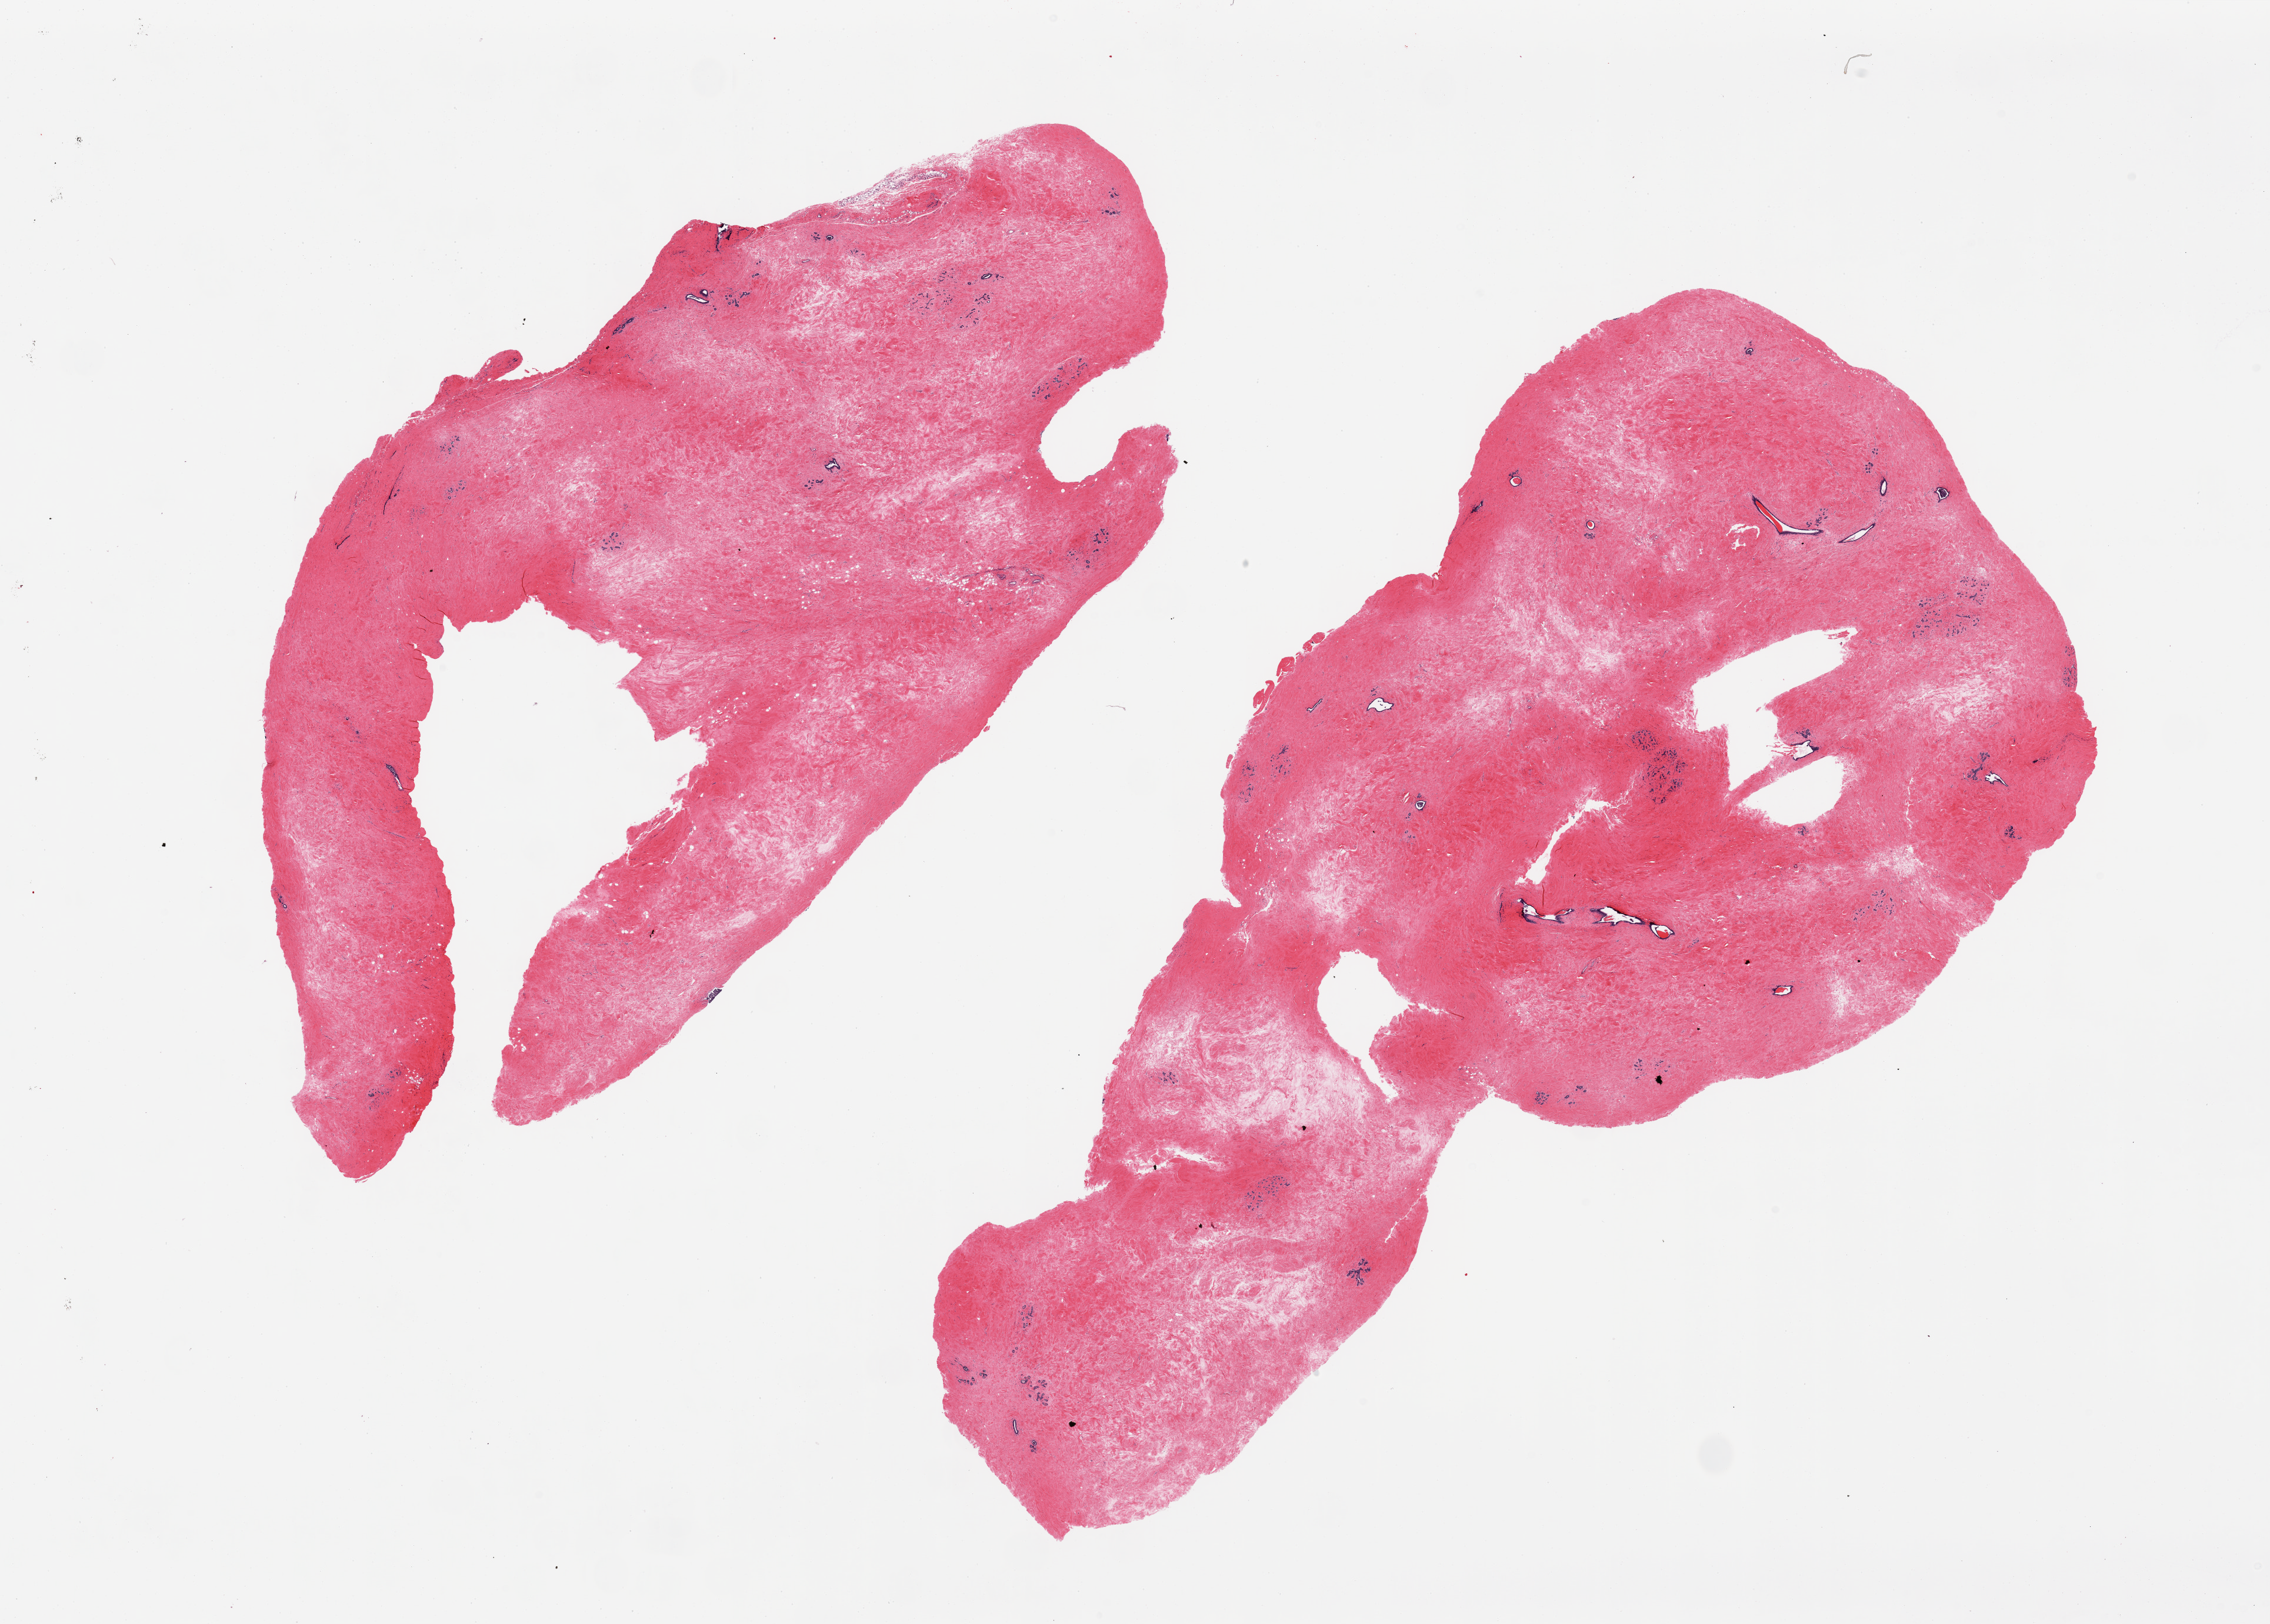
Whole-slide image, hematoxylin and eosin (H&E) stain, brightfield, low-resolution overview of the scanned area, about 30.5 x 21.8 mm. PAXgene-fixed paraffin-embedded (PFPE) section. Sampled site (target tissue): breast. Donor tissue sample. Female donor.
Pathologist's review note for this sample: 2 pieces, mostly fibrous stroma with sparsely scattered glandular component.